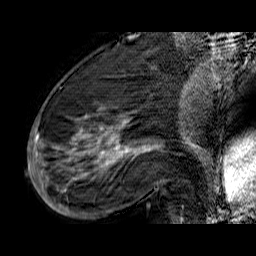
Breast MRI (dynamic contrast-enhanced), one sagittal slice. Position 22 of 60 along the scan axis. Dynamic contrast-enhanced series, time point 2 of 6 at this slice position (early post-contrast). 1.5 T. TE 6.5 ms, TR 32.9 ms. 4 mm slice thickness. 256 × 256 image matrix. Female patient. Case-level facts recorded for this patient, not image findings: setting: breast cancer imaged before/during neoadjuvant chemotherapy; receptor status: HR-positive, HER2-negative.
Outlined on this slice (semi-automatically segmented with operator editing):
- analysis volume of interest (the breast-tissue region the enhancement analysis was run in; not a lesion): bounding box [x1, y1, x2, y2] px = [33, 74, 176, 210]
- tumour enhancement mask (voxels above the 100 % enhancement threshold inside the analysis volume of interest): [33, 107, 148, 208]